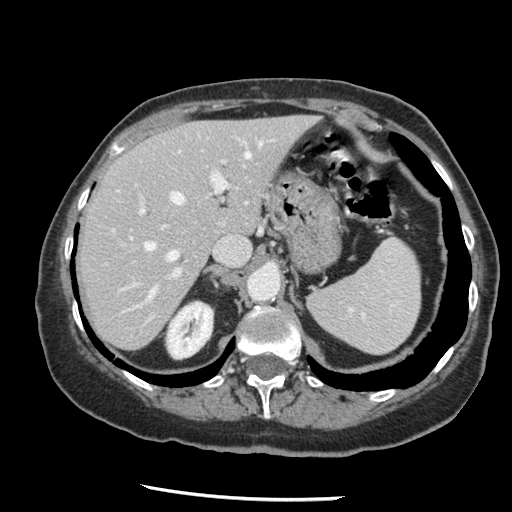
Contrast-enhanced abdominal CT, one axial slice. Slice 95 of 148 in the series (ordered by position). 120 kVp. Intravenous contrast given. Soft-tissue window (W 400 / L 40 HU). 2.5 mm slice thickness. 512 × 512 image matrix. Female patient, age 85 years. Case-level facts recorded for this patient, not image findings: diagnosis: colorectal cancer liver metastases, imaged before liver resection; multiple liver metastases: no; largest metastasis: 0.9 cm; disease in both lobes: no.
Annotated regions visible in this slice (outlined manually by an expert reader):
- hepatic veins: bounding box <116,139,276,300> (left, top, right, bottom; pixels)
- liver: <80,117,316,349>
- planned liver remnant (the part of the liver to remain after resection): <80,117,316,349>
- portal vein (with intrahepatic branches): <122,159,230,290>